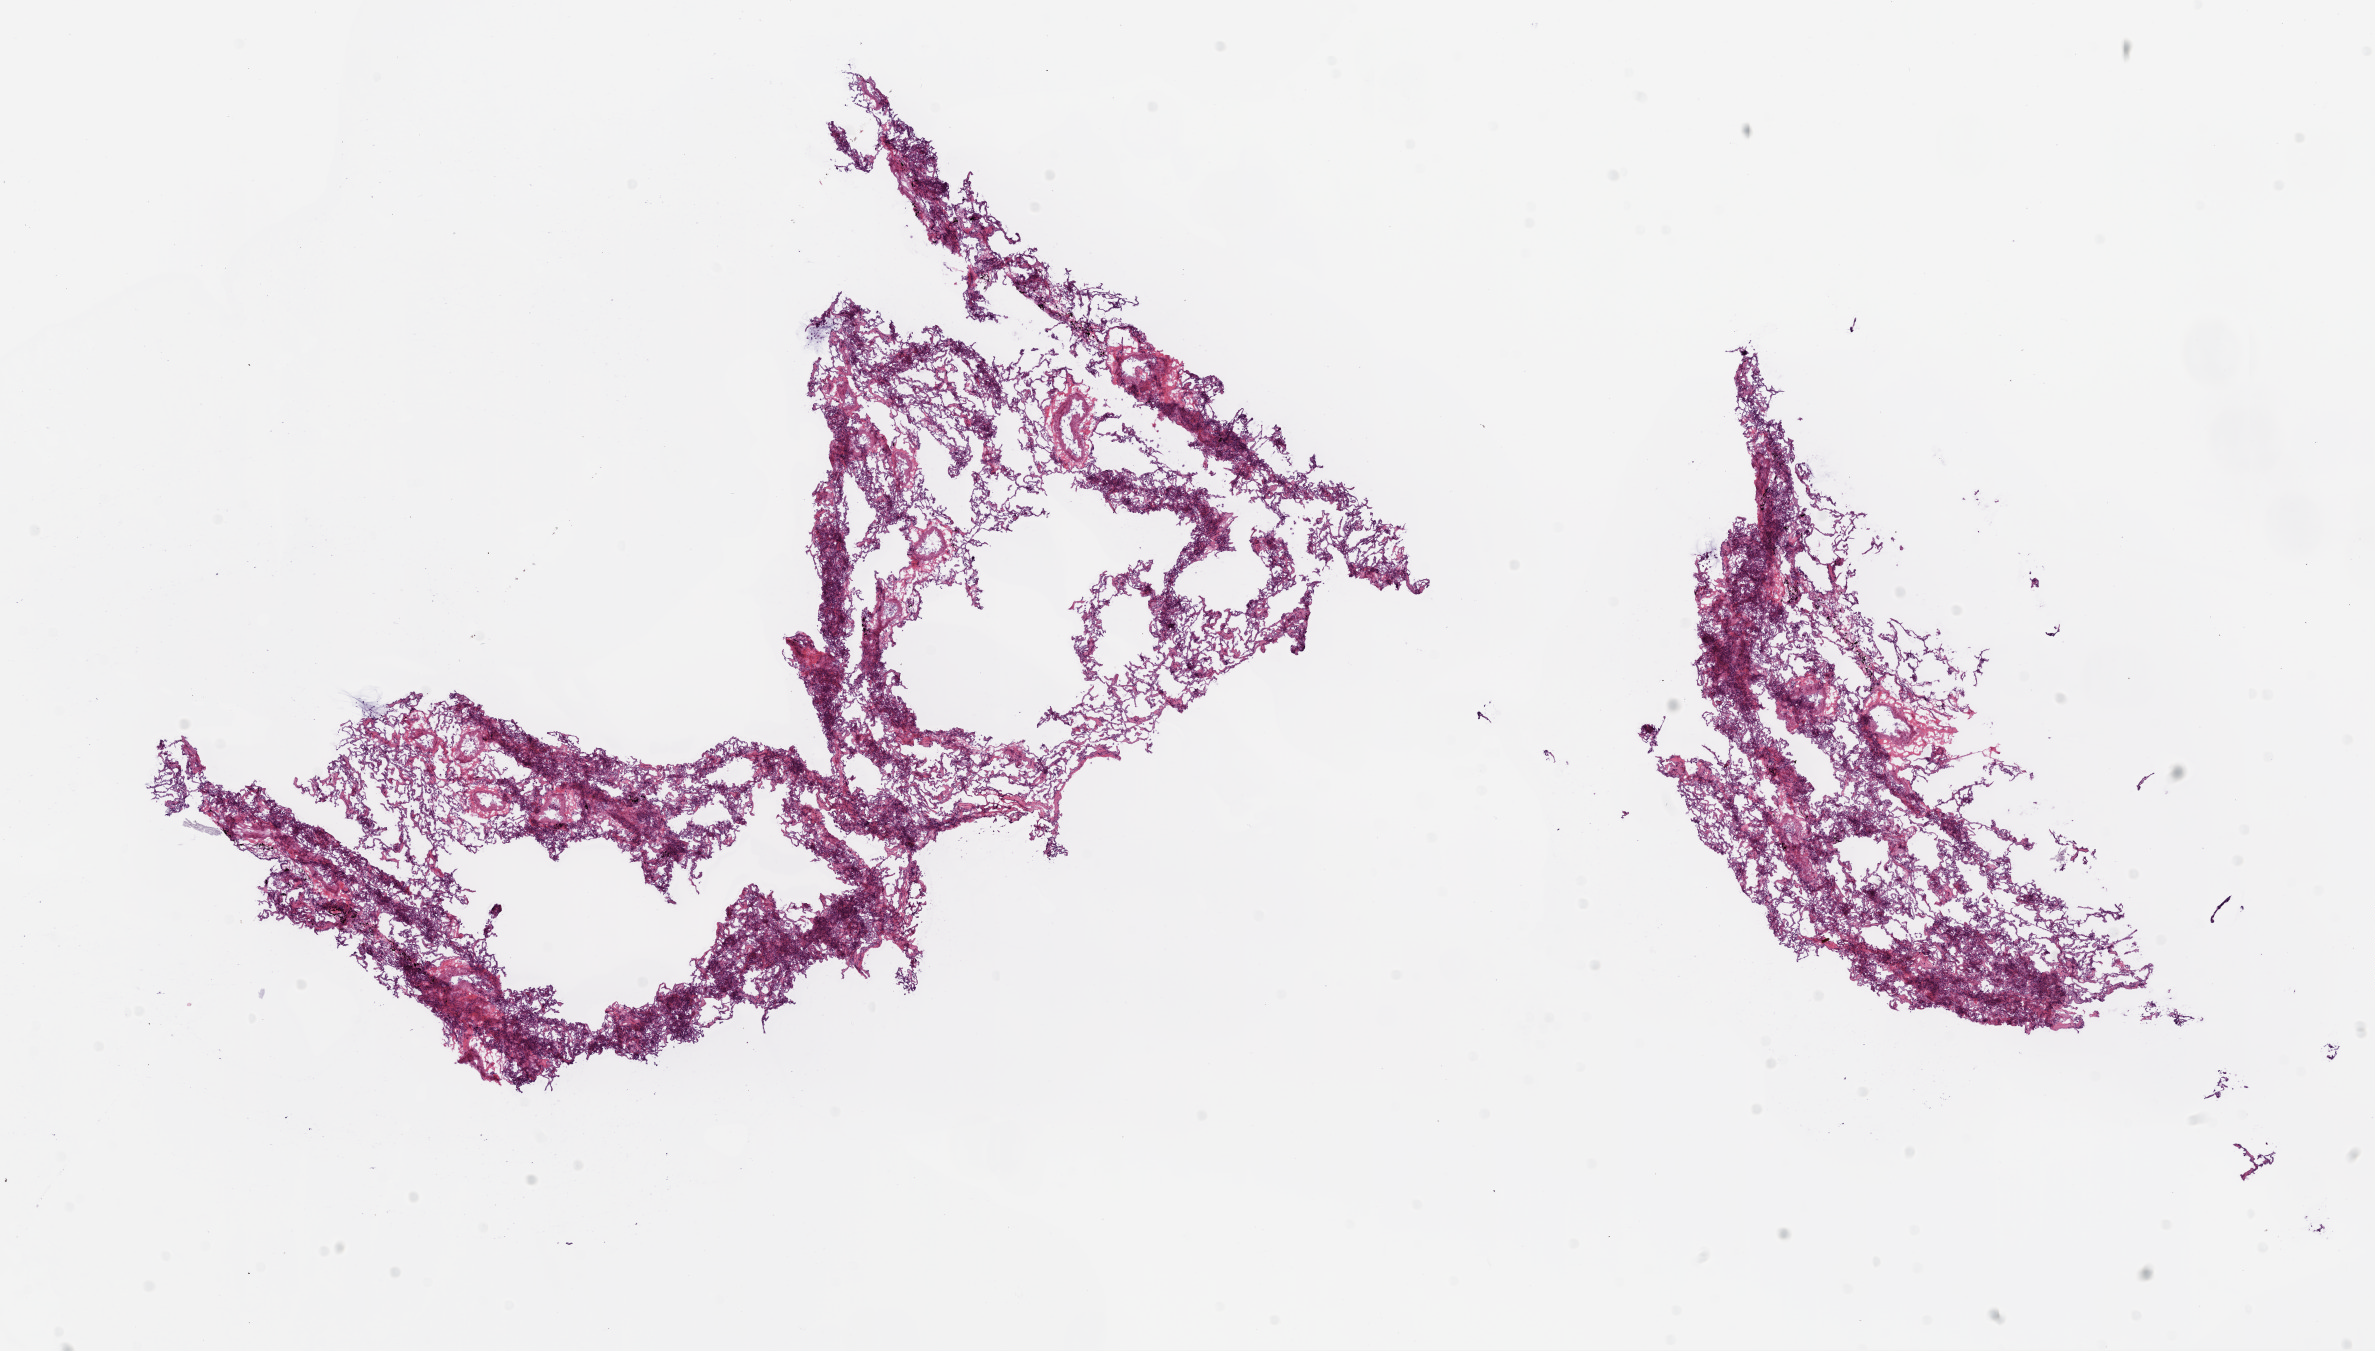
Hematoxylin and eosin (H&E) stained whole-slide image, low-resolution overview of the scanned area, about 19.1 x 10.8 mm (acquisition: 20x scan). Frozen section from the top of the tissue portion. Lung, solid tissue normal (non-tumour tissue) sample. Male patient; age at initial diagnosis 65 years.
This section: solid tissue normal (non-tumour) sample from the same patient. Patient diagnosis: Squamous cell carcinoma, NOS.